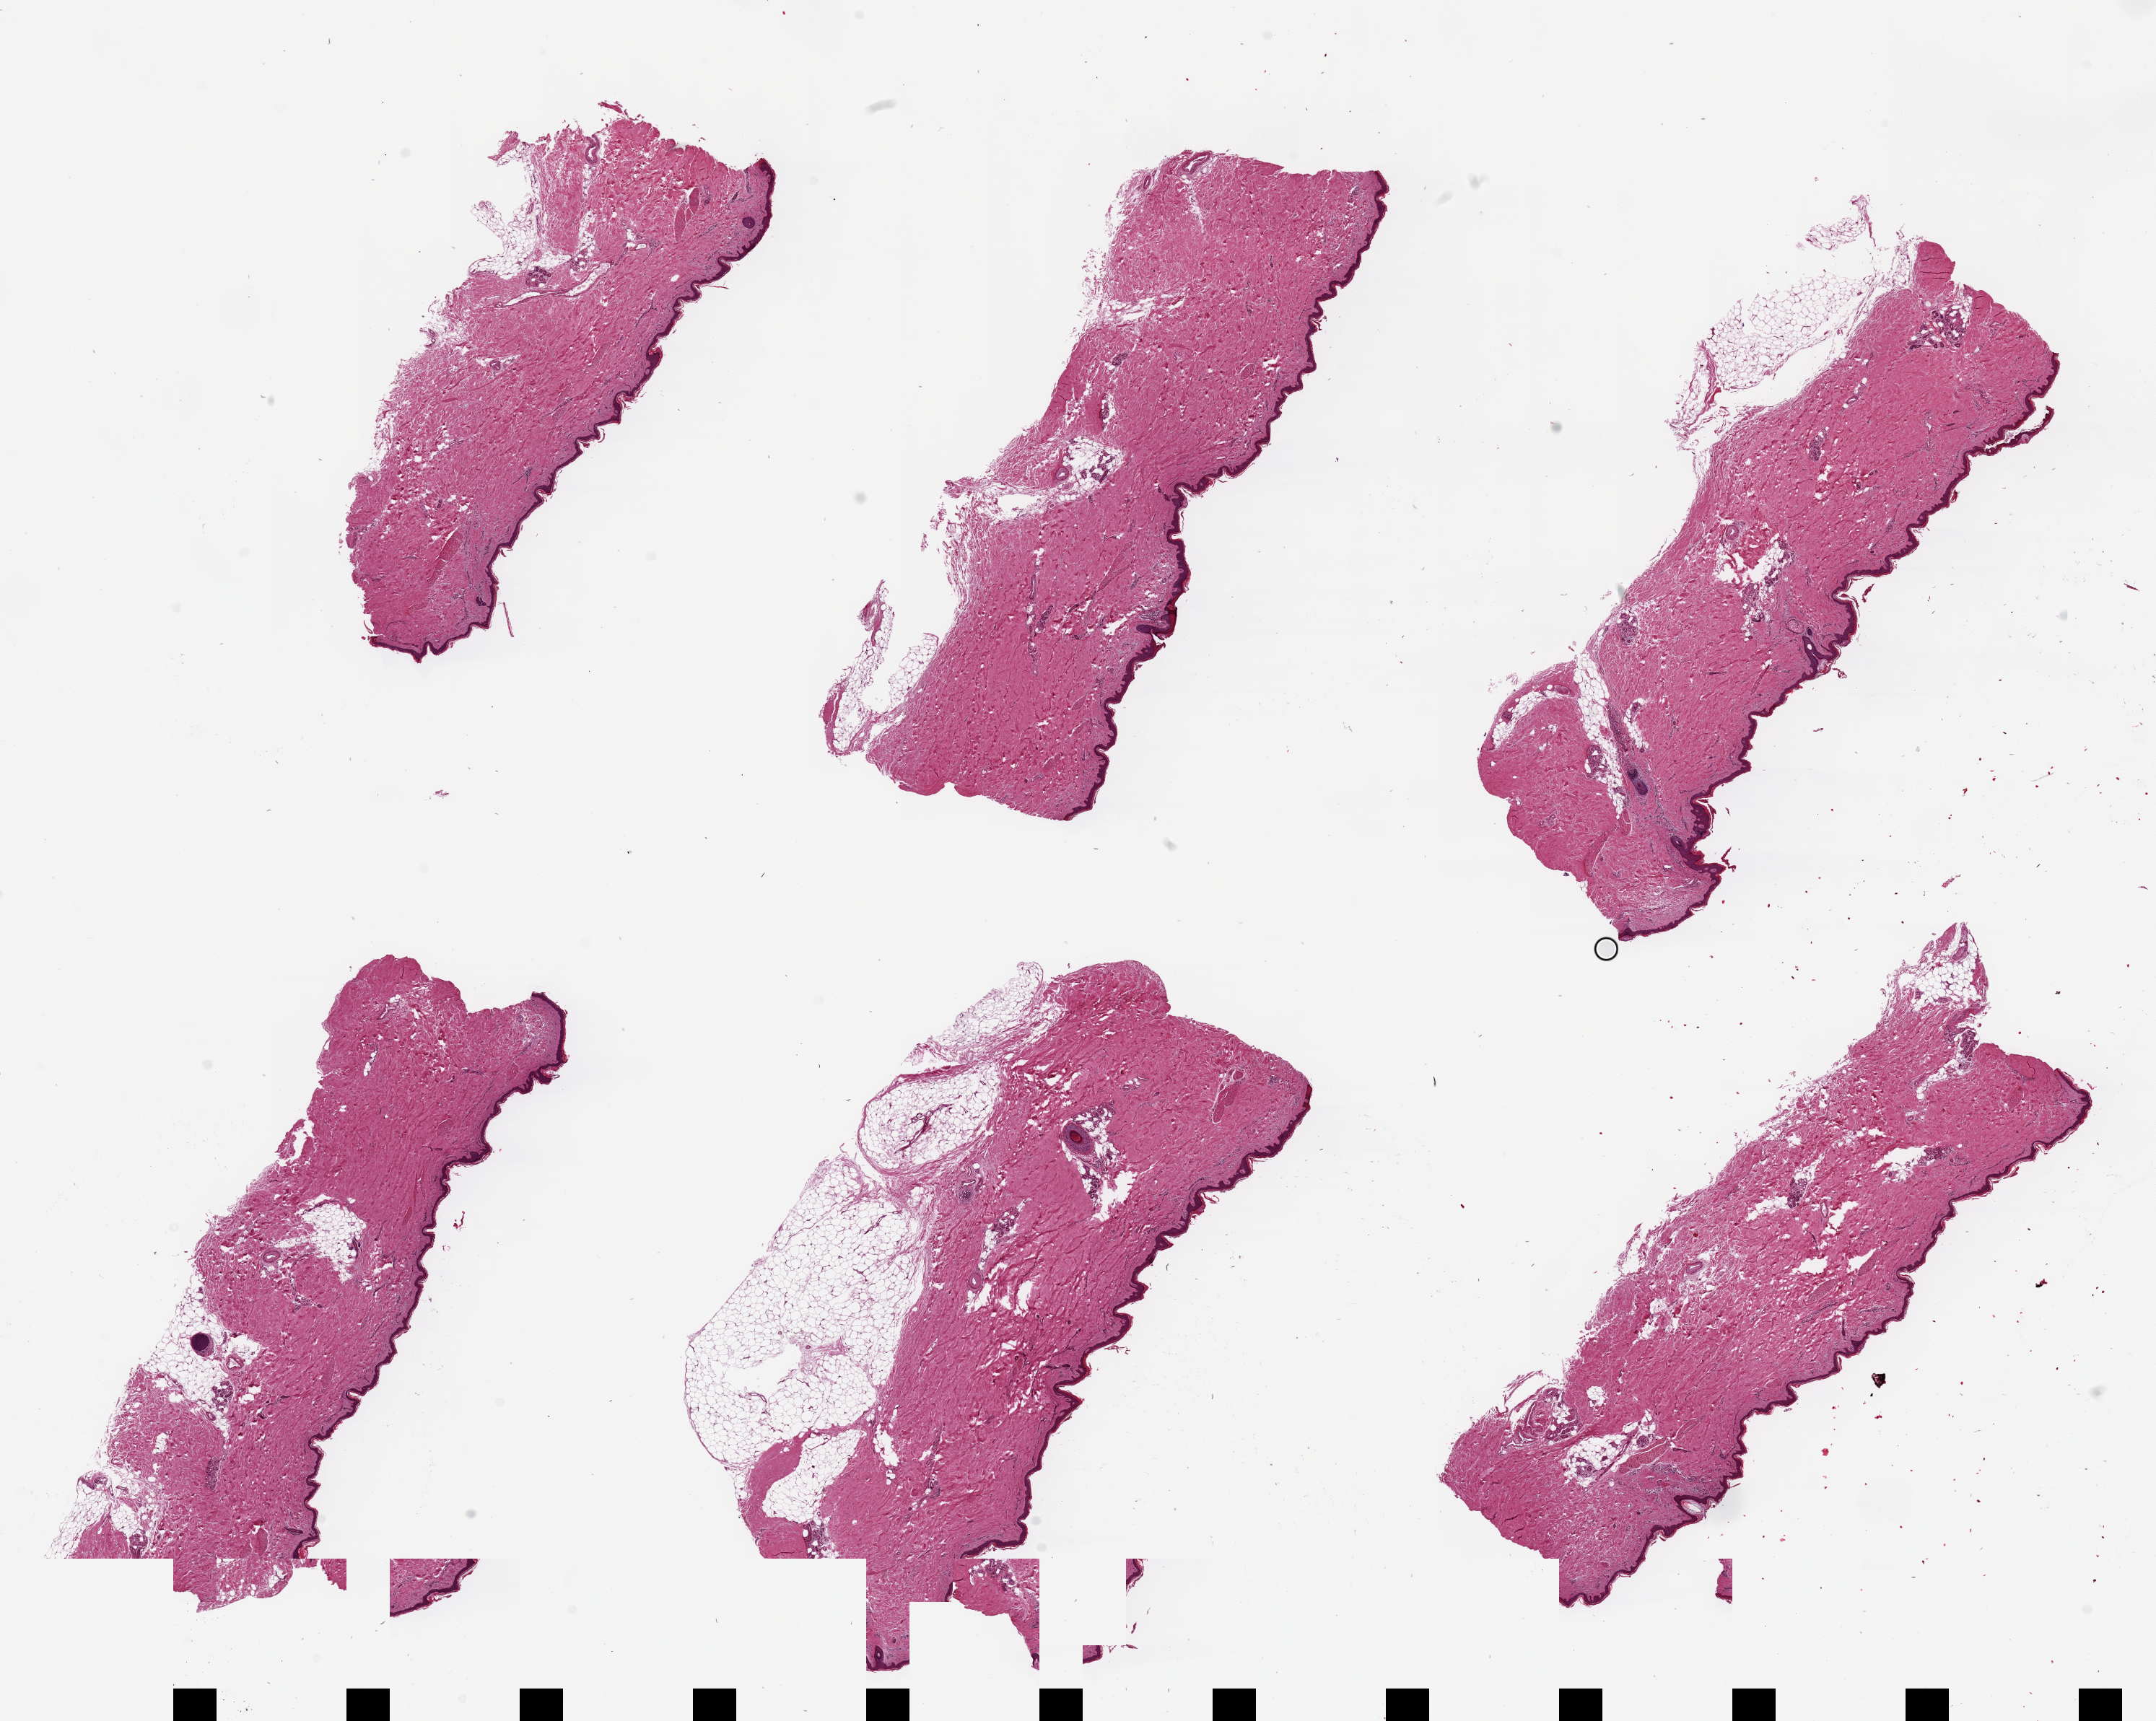
Whole-slide image, hematoxylin and eosin (H&E) stain, whole scanned area (about 23.6 x 18.9 mm) shown as a low-resolution overview; PAXgene-fixed paraffin-embedded (PFPE) section; target tissue: skin of lower leg; donor tissue sample.
Pathologist's review note for this sample: 6 pieces ~8x2.5mm, squamous epithelium is ~2-3% of thickness.